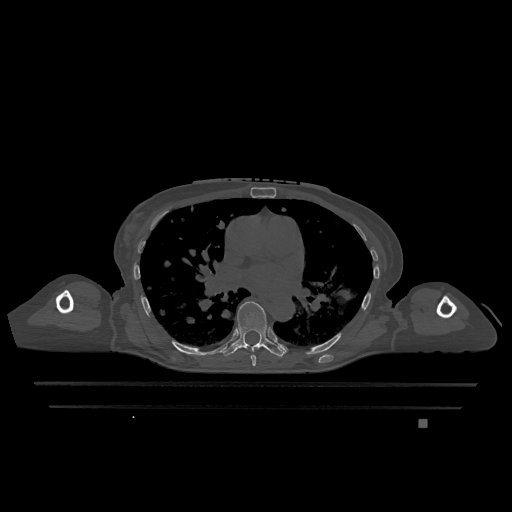
CT including the spine, one axial slice; position 753 of 1317 along the scan axis; bone window (W 1800 / L 400 HU); 512 × 512 image matrix, field of view 500 × 500 mm. Patient: female, 74 years. From the clinical record (not read from this slice): primary cancer: lung.
Structures marked on this image (semi-automatic segmentation, software-assisted and operator-edited):
- T6 vertebra: box from (x=250, y=355) to (x=256, y=366) px
- T7 vertebra: (x=221, y=301)–(x=286, y=357)